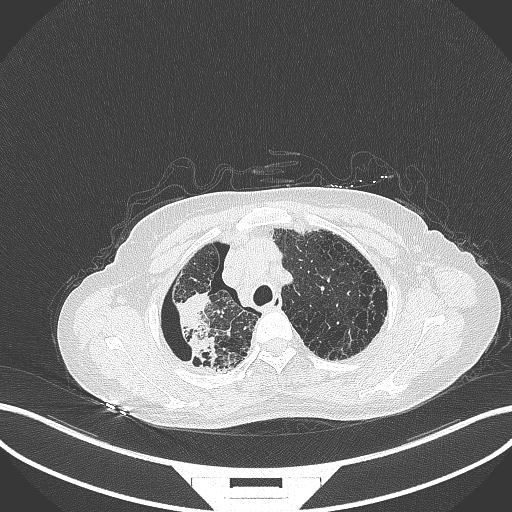
Chest CT, one axial slice. Slice 291 of 408 in the series (ordered by position). Reconstruction kernel B70f. 120 kVp. Lung window (W 1500 / L -600 HU). 1 mm slice thickness. 512 × 512 image matrix. Female patient, age 64 years. Case-level facts recorded for this patient, not image findings: clinical TNM (as recorded): T3 N3 M0.
Annotated regions visible in this slice (bounding box drawn by a radiologist):
- lung tumour (recorded histology: squamous cell carcinoma): bounding box [x1, y1, x2, y2] px = [166, 287, 223, 369]